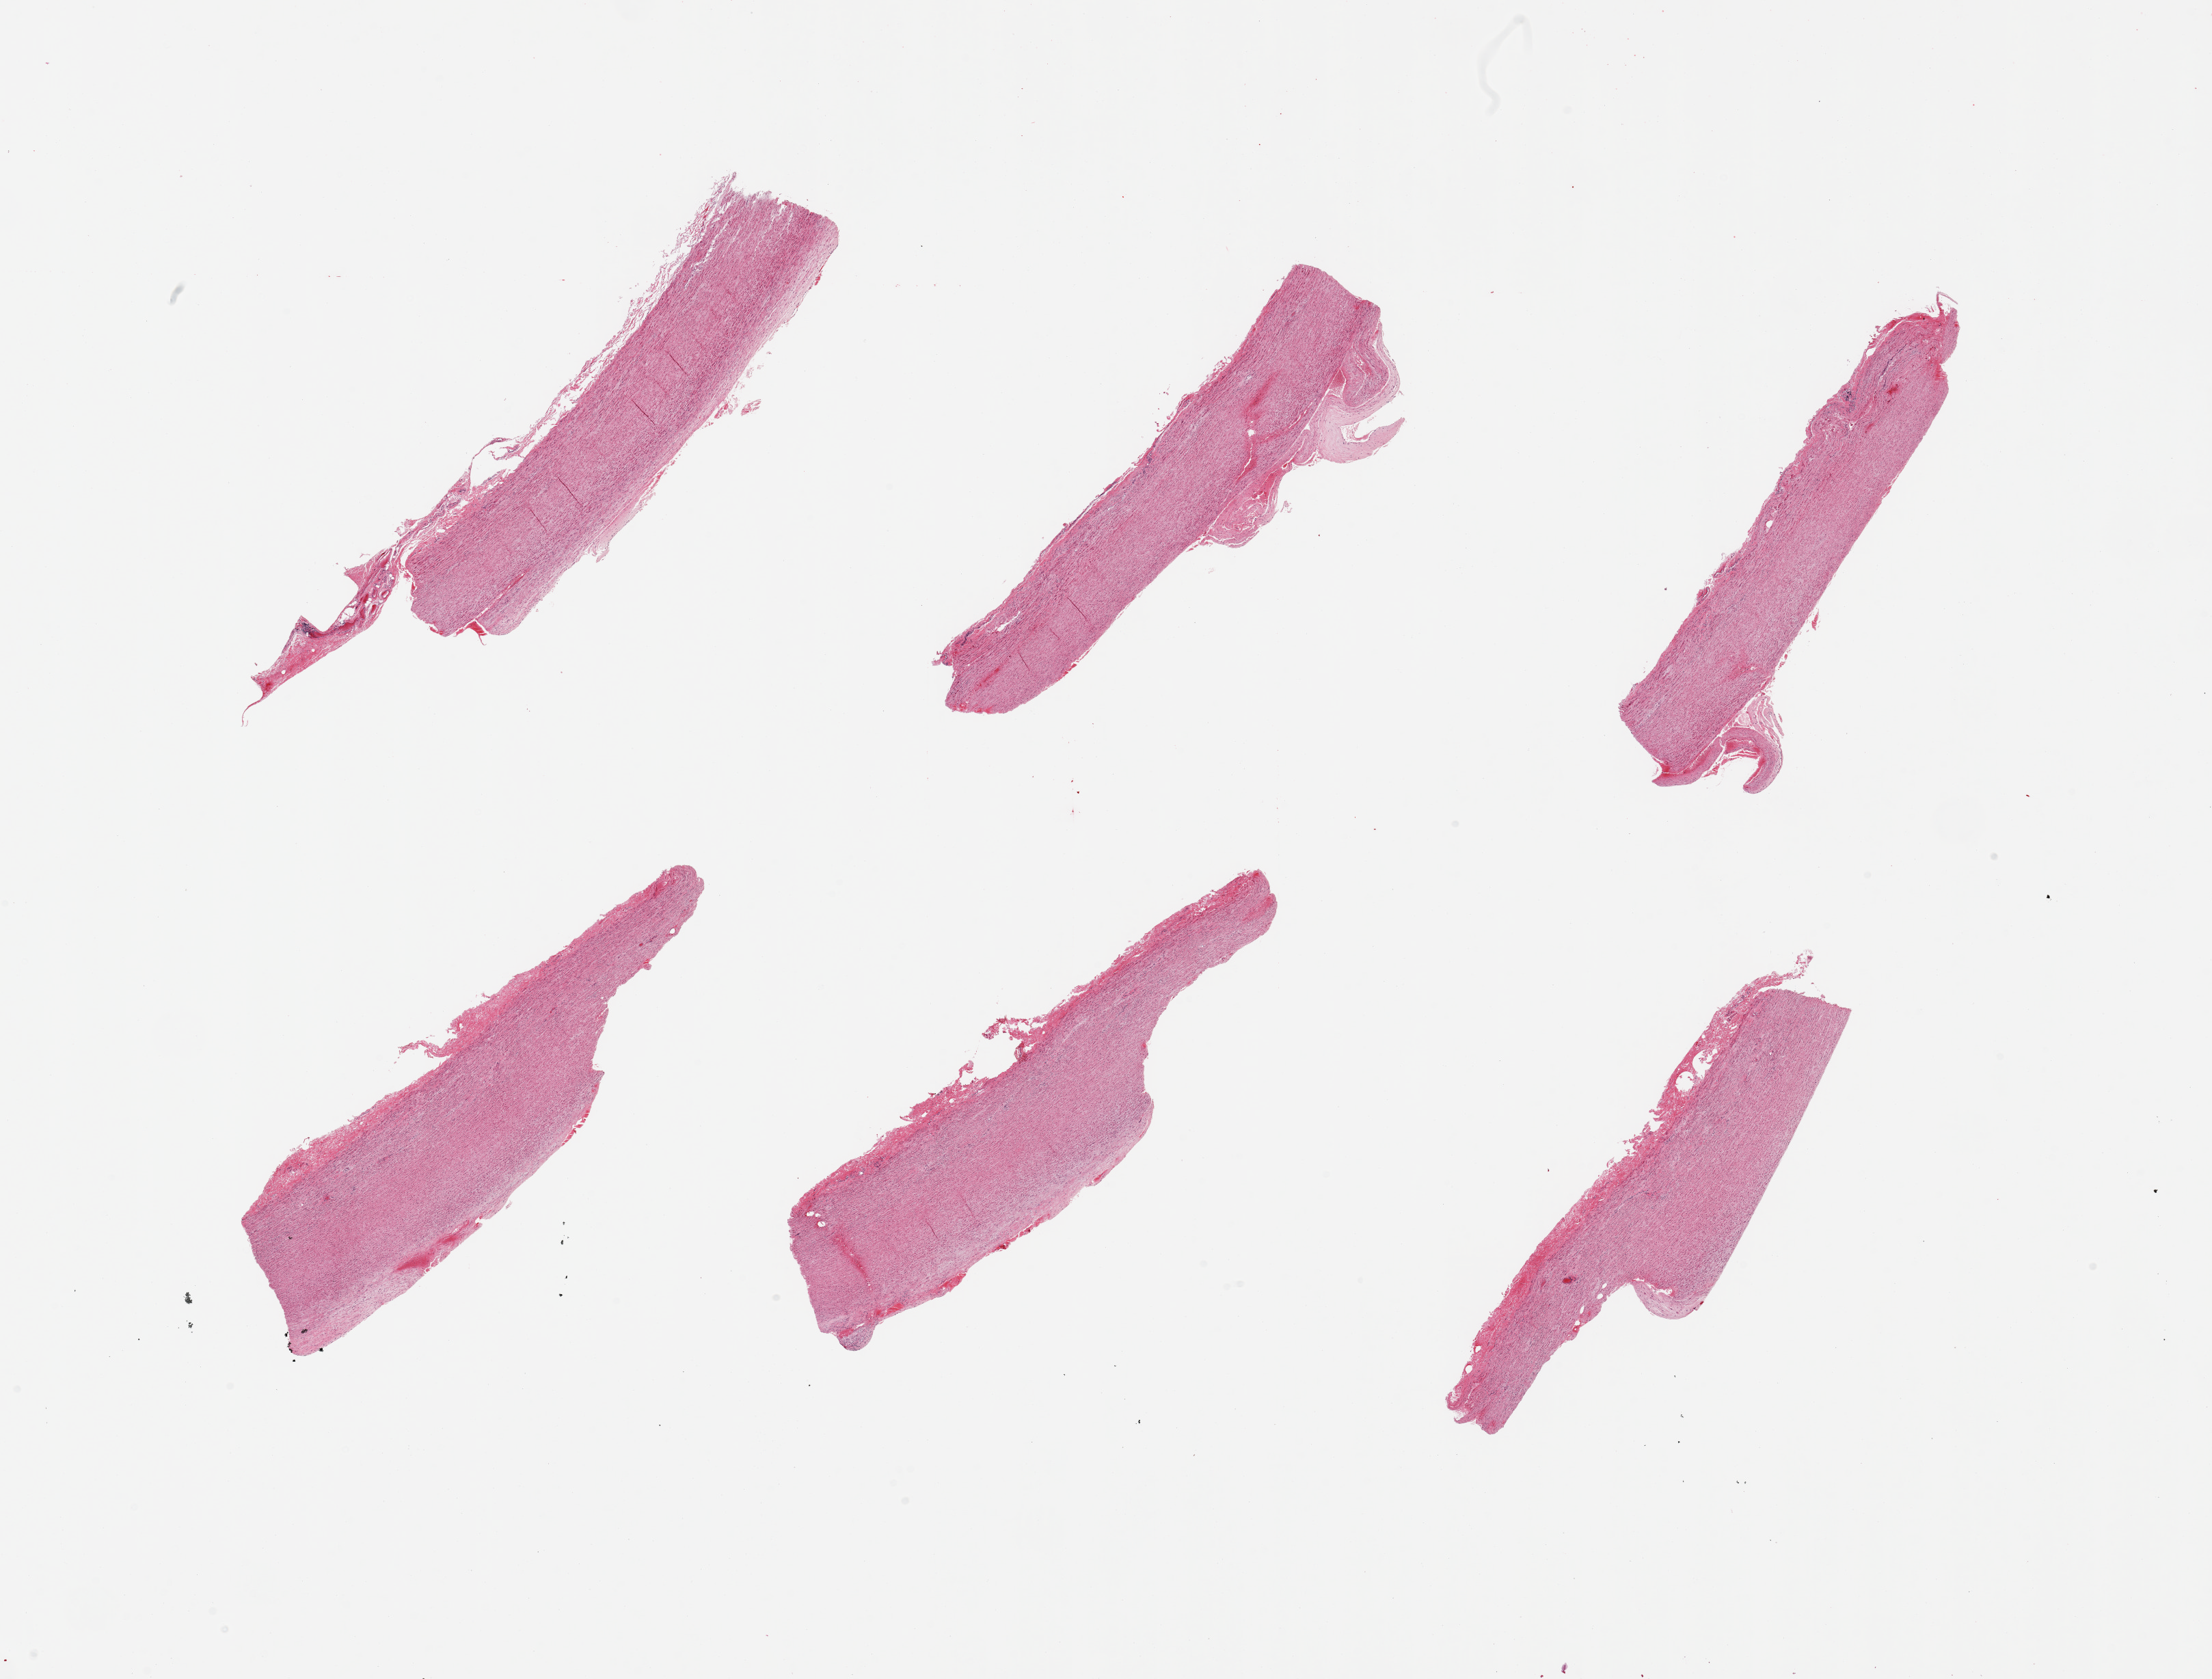
Whole-slide image, hematoxylin and eosin (H&E) stain, a low-resolution overview of the entire scanned area, about 25.6 x 19.4 mm (from a 20x scan); PAXgene-fixed paraffin-embedded (PFPE) section; sampled site (target tissue): aorta; donor tissue sample. Donor sex: male.
Review note (as recorded): 6 pieces; plaques and hemorrhages.